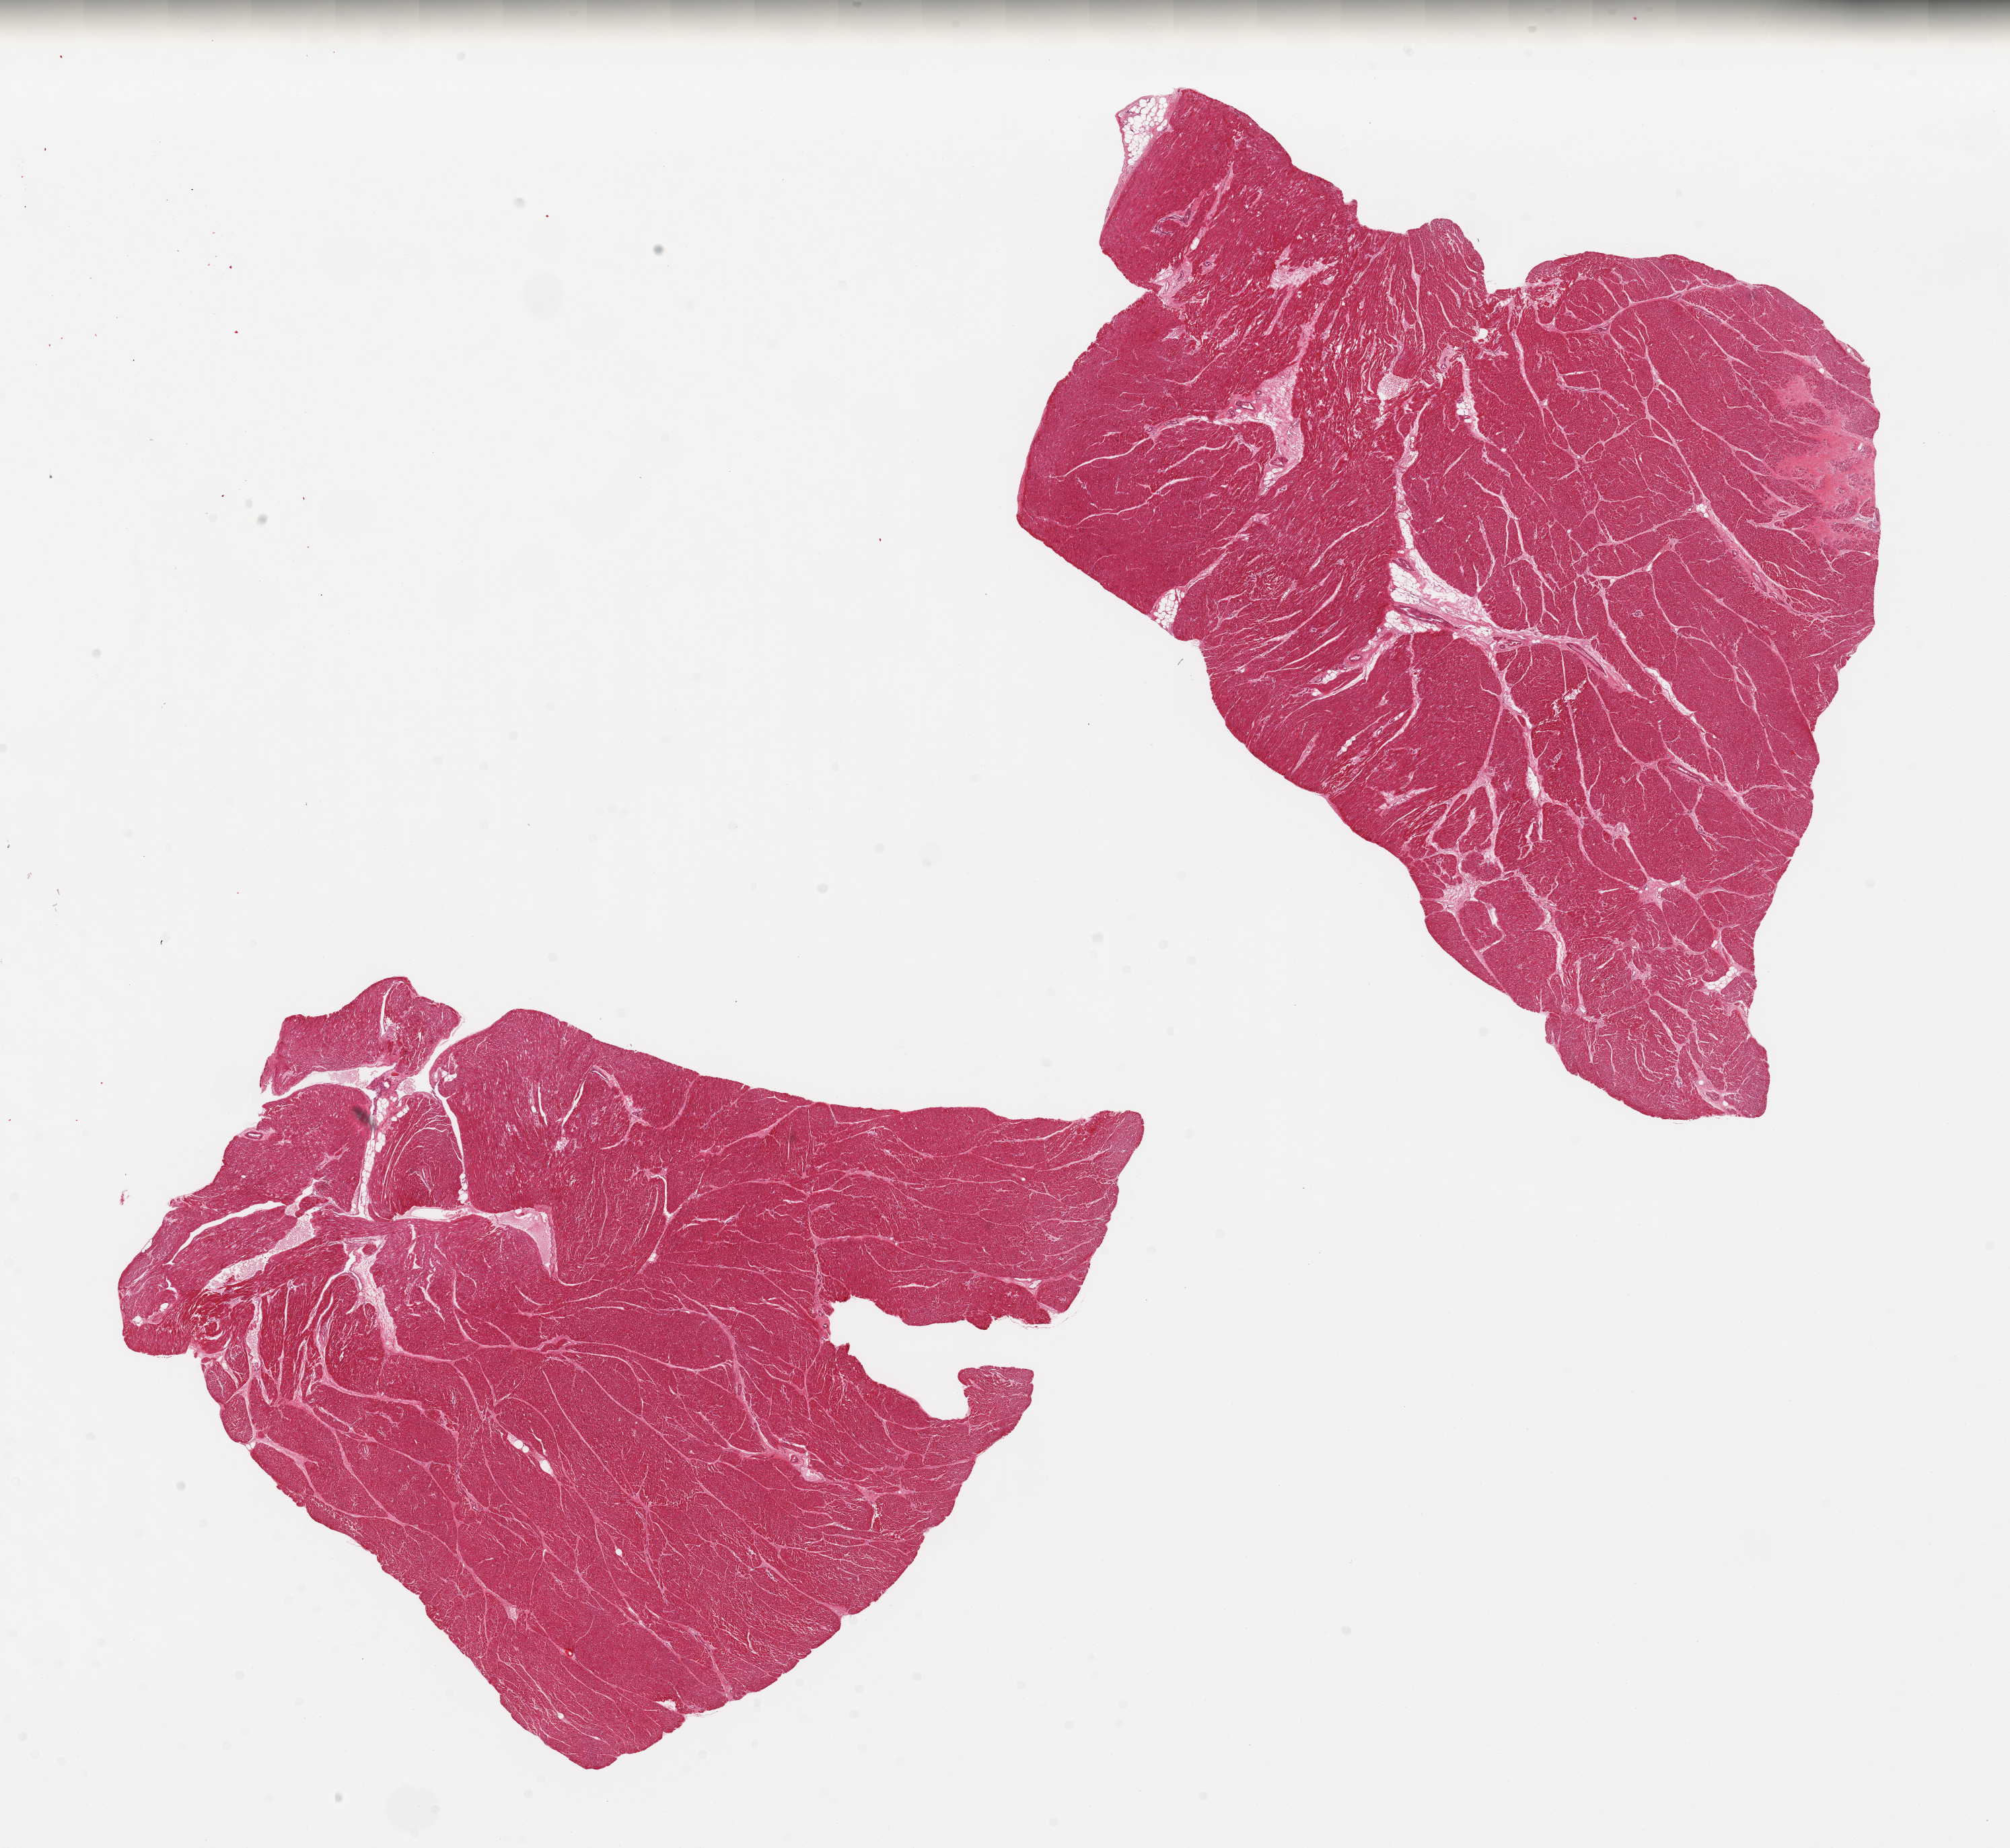
Digitized H&E-stained section, brightfield, whole scanned area (about 23.6 x 21.7 mm, slide scanned at 20x) shown as a low-resolution overview, PAXgene-fixed paraffin-embedded (PFPE) section, sampled site (target tissue): heart, tissue donor sample. Donor: male.
Pathologist's review note for this sample: 2 pieces; 5% of 1 piece contains a fibrous scar consistent with old infarct.